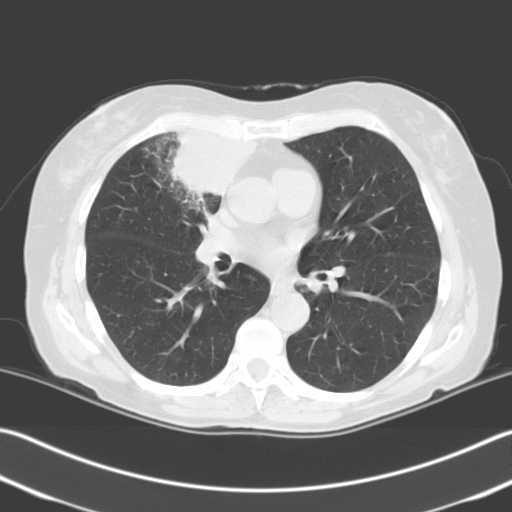
Low-dose screening chest CT, one axial slice. Slice 118 of 204 in the series (ordered by position). Lung window (W 1500 / L -600 HU). 3.2 mm slice thickness. 512 × 512 image matrix, field of view 348 × 348 mm.
Structures marked on this image (manually delineated by an expert):
- lesion 1 (tumor, upper lobe of right lung): bounding box [x1, y1, x2, y2] px = [171, 131, 255, 203]